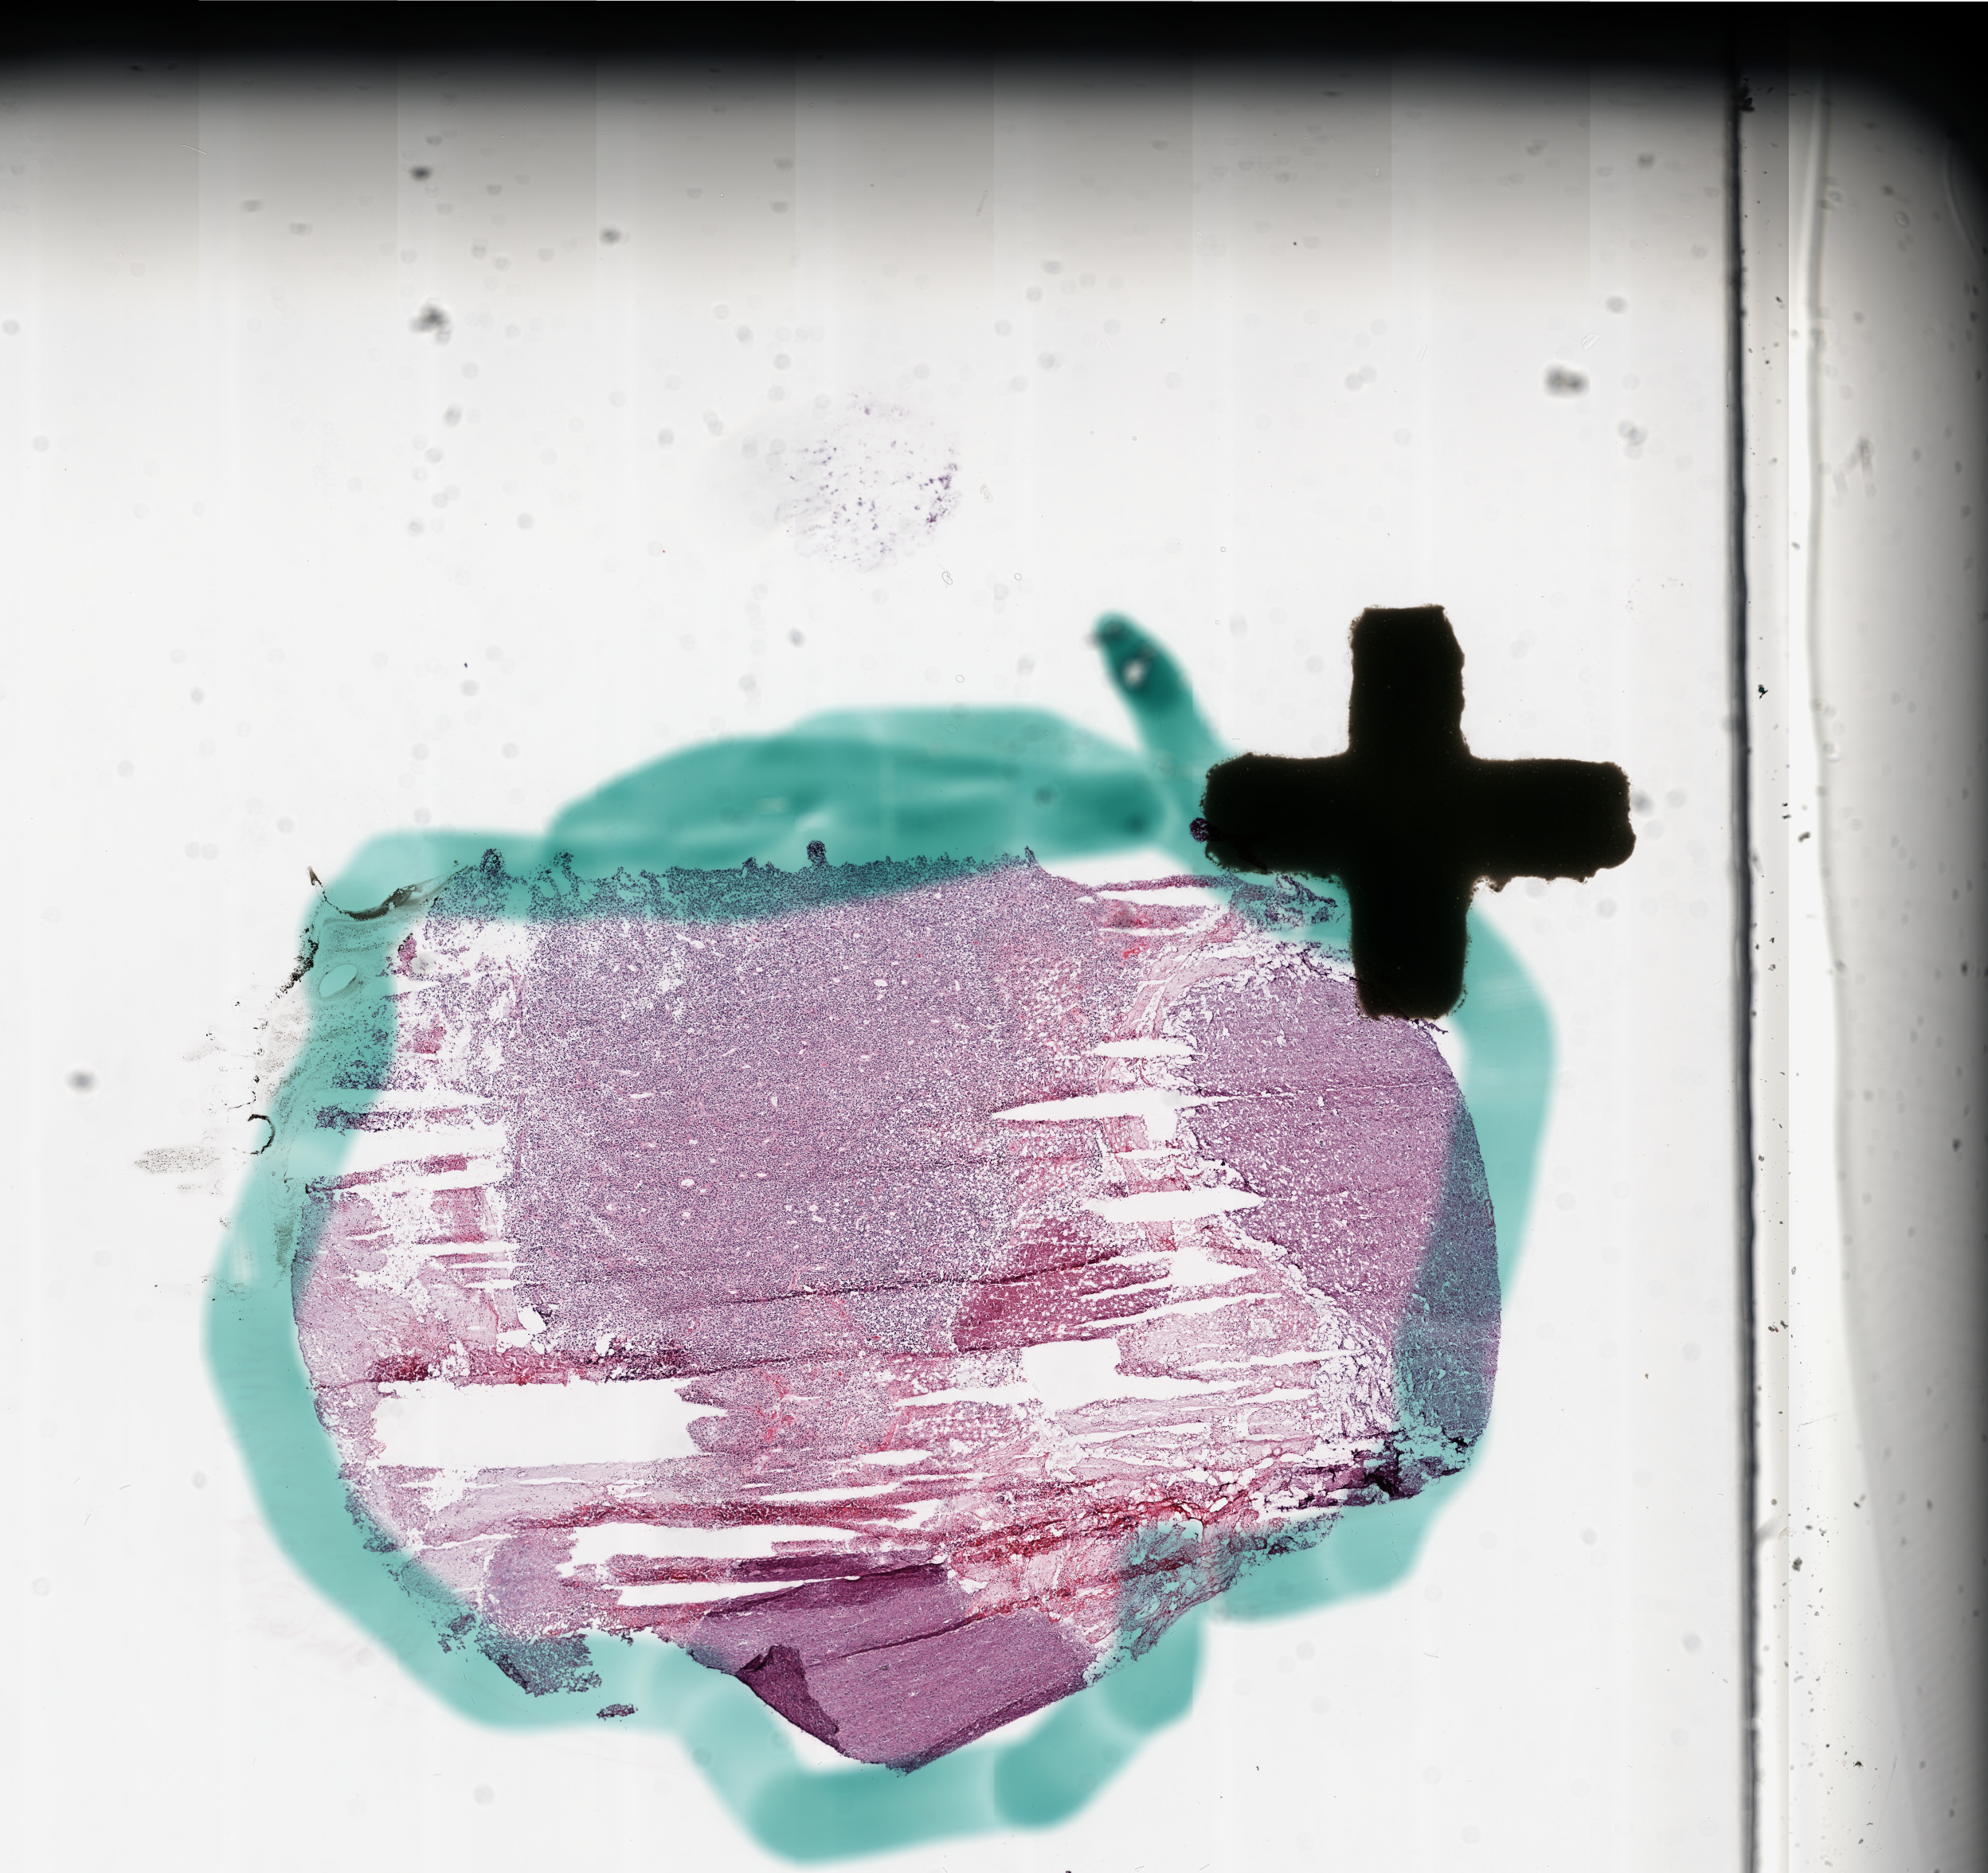
Digitized H&E tissue section (whole slide) — a low-resolution overview of the entire scanned area, about 10.0 x 9.4 mm (from a 20x scan), frozen section from the bottom of the tissue portion, sample: primary tumour, brain. Female patient; age at initial diagnosis 59 years. Pathologist review of this section (percent, as recorded): tumour cells 40%, tumour nuclei 90%, normal cells 0%, stromal cells 30%, necrosis 30%.
• histologic diagnosis: Glioblastoma